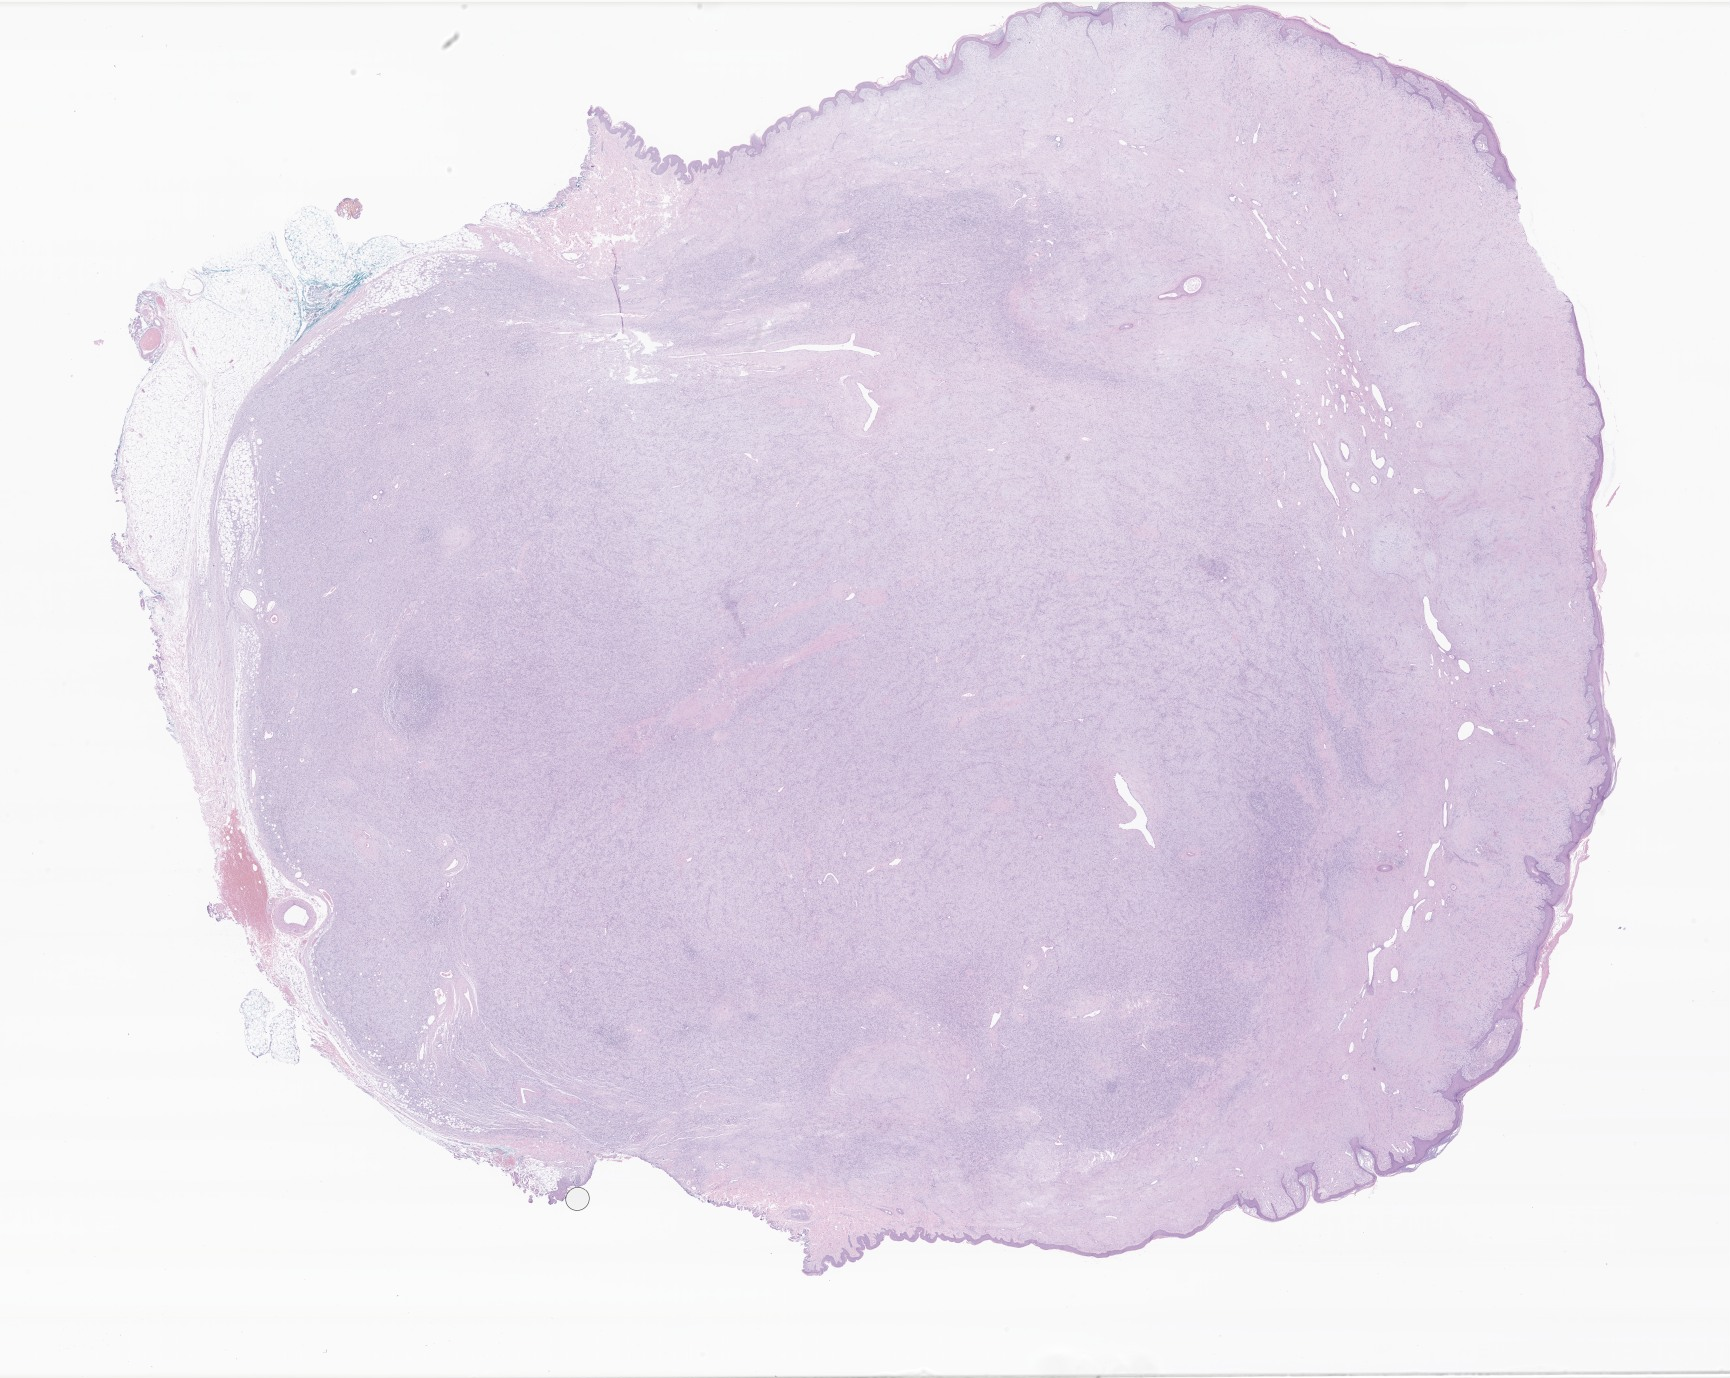
Whole-slide image, H&E stain of tumor tissue from the soft tissue of lower extremity — shown as a low-resolution overview of the whole scanned area (about 29.2 x 23.2 mm). FFPE section. Male patient, age 231 months (19 years 3 months).
Diagnosis (ICD-O-3 morphology term): Dermatofibrosarcoma protuberans, fibrosarcomatous.